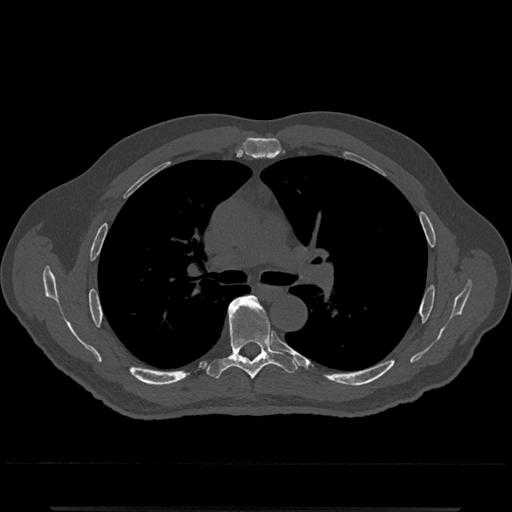
CT including the spine, one axial slice; reconstruction kernel Br40s/3; 120 kVp; bone window (W 1800 / L 400 HU); 0.5 mm slice thickness; 512 × 512 image matrix. Male patient, age 67 years. Case-level facts recorded for this patient, not image findings: primary cancer: prostate.
Outlined on this slice (semi-automatic segmentation, software-assisted and operator-edited):
- T5 vertebra: bounding box <254,297,257,301> (left, top, right, bottom; pixels)
- T6 vertebra: <207,296,298,380>